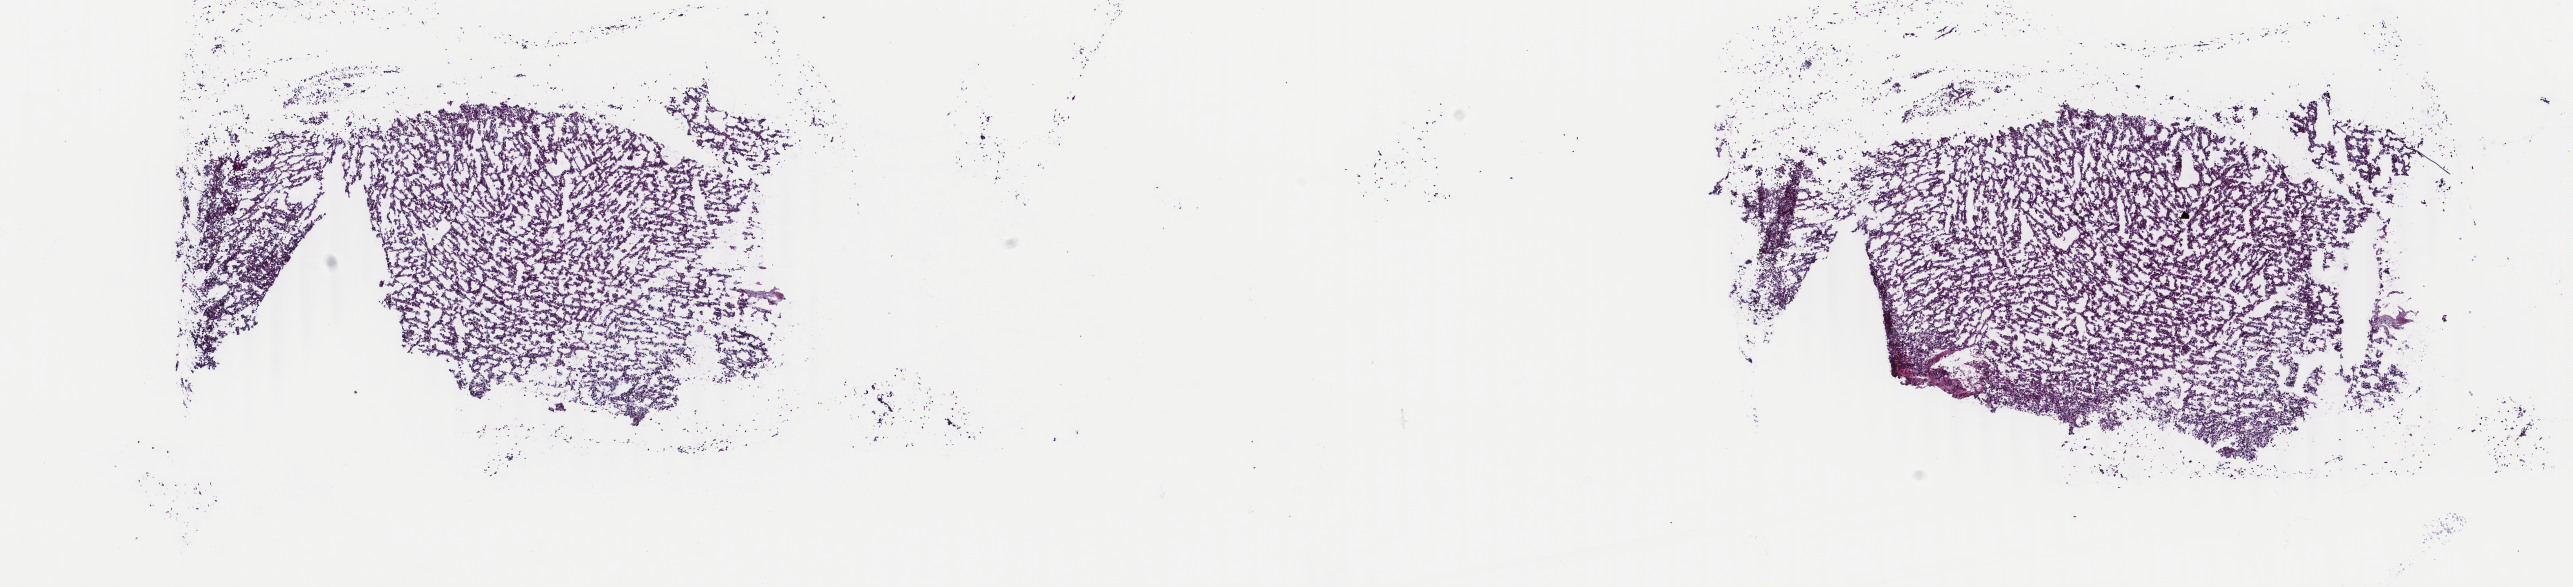
Whole-slide histology image, Hematoxylin and eosin (H&E) stained, low-resolution overview of the scanned area, about 20.5 x 4.7 mm. Frozen section from the top of the tissue portion. Sample: primary tumour, adrenal cortex. Patient: male, age at initial diagnosis 52 years. Pathologist review of this section (percent, as recorded): tumour cells 90%, tumour nuclei 90%, normal cells 0%, stromal cells 0%, necrosis 10%. Infiltration values recorded for this section: lymphocyte infiltration 40%, monocyte infiltration 20%, neutrophil infiltration 20%.
Laterality: left. Histologic diagnosis: Adrenal cortical carcinoma (cortex of adrenal gland).